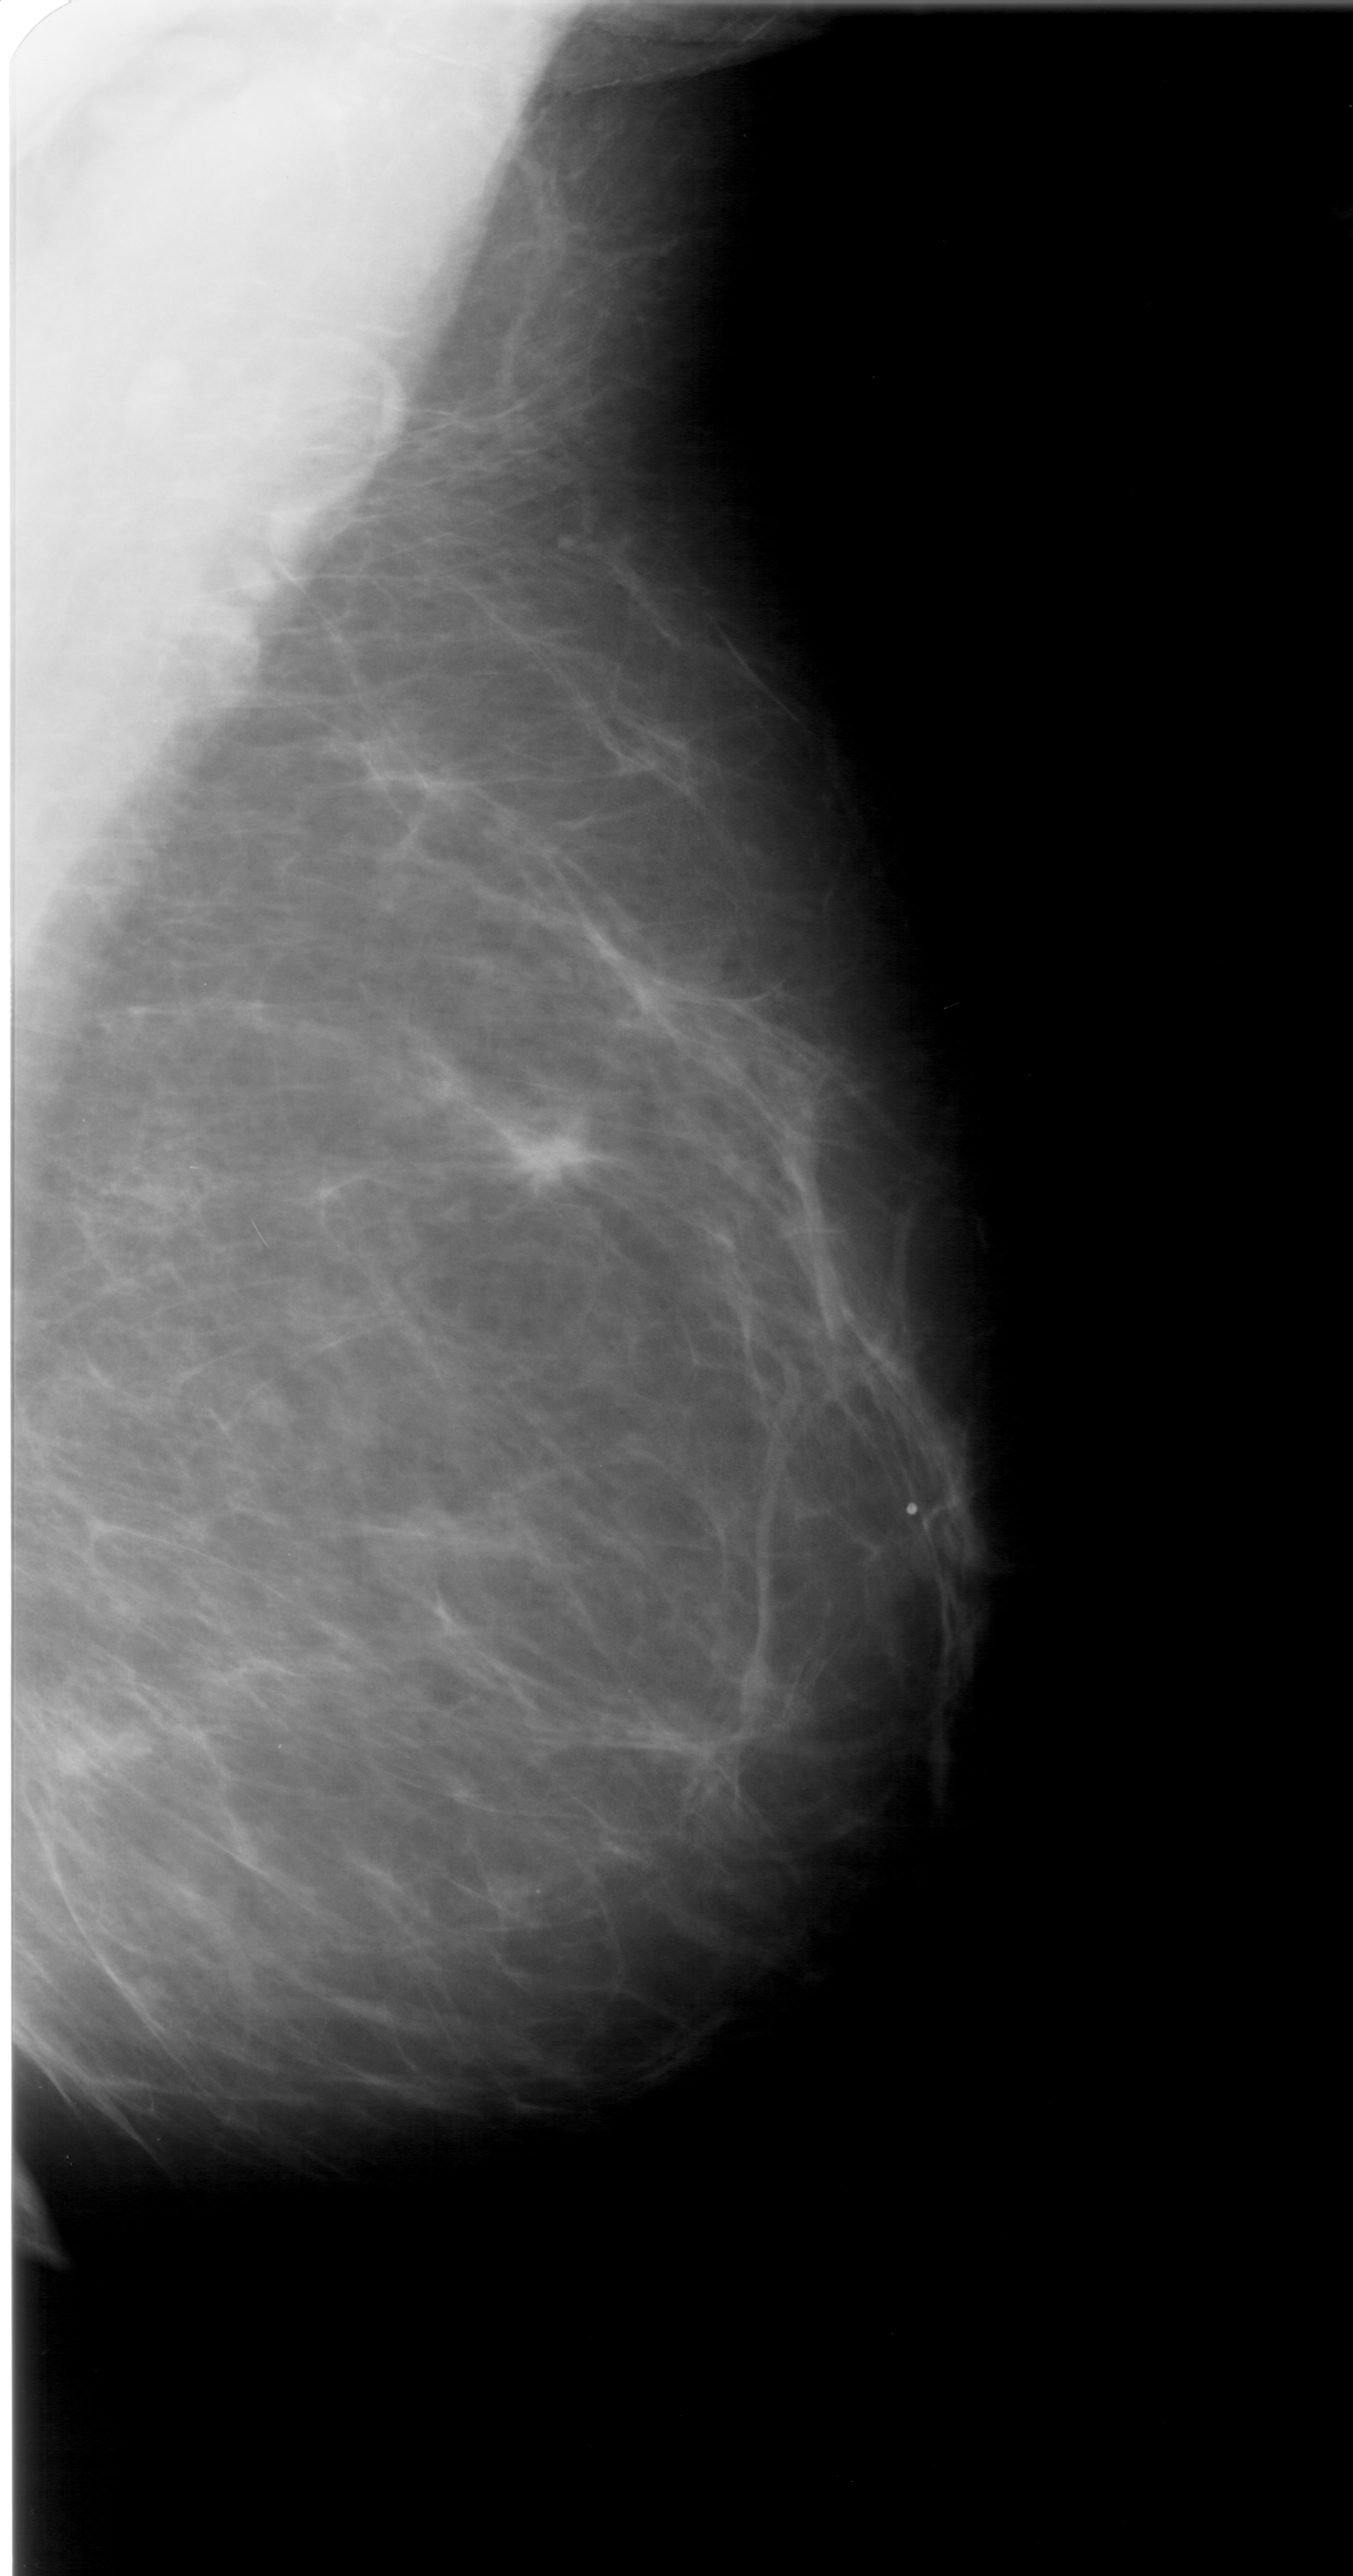
Scanned film-screen mammogram; right breast; mediolateral oblique (MLO) view; 1353 × 2576 image matrix.
Expert-marked regions of interest on this image (one box per marked abnormality):
- mass, shape irregular, margins spiculated; BI-RADS assessment category 5; pathology result (as recorded, not read from the image): malignant: box from (x=482, y=1108) to (x=612, y=1219) px